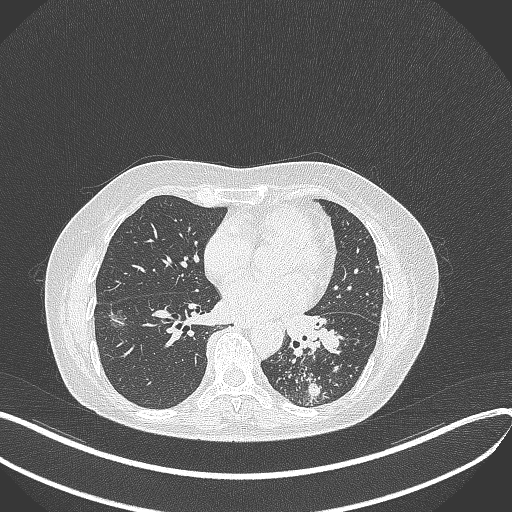
Chest CT, one axial slice. Position 176 of 429 along the scan axis. Reconstruction kernel B70f. Lung window (W 1500 / L -600 HU). 1 mm slice thickness. 512 × 512 image matrix, field of view 400 × 400 mm. Patient: female, 63 years. From the clinical record (not read from this slice): clinical TNM (as recorded): T1b N0 M0.
Annotated regions visible in this slice (rectangle marked by the reading radiologist):
- lung tumour (recorded histology: adenocarcinoma): box from (x=282, y=305) to (x=346, y=357) px